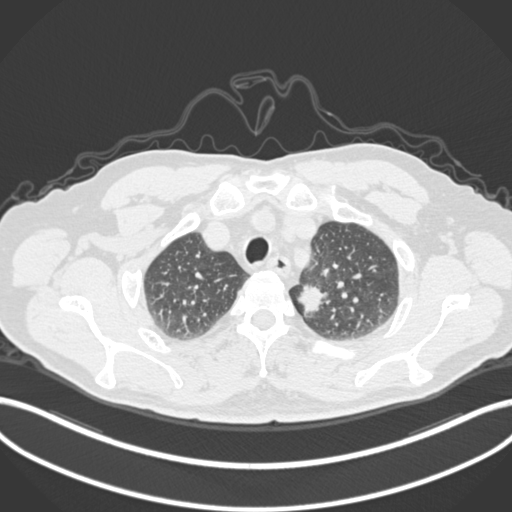
Chest CT, one axial slice; position 271 of 306 along the scan axis; 120 kVp; lung window (W 1500 / L -600 HU); 1 mm slice thickness; 512 × 512 image matrix, field of view 400 × 400 mm. Patient: male, 64 years. Case-level facts recorded for this patient, not image findings: clinical TNM (as recorded): T1c N0 M0.
Outlined on this slice (rectangle marked by the reading radiologist):
- lung tumour (recorded histology: adenocarcinoma): bounding box [x1, y1, x2, y2] px = [294, 275, 330, 320]